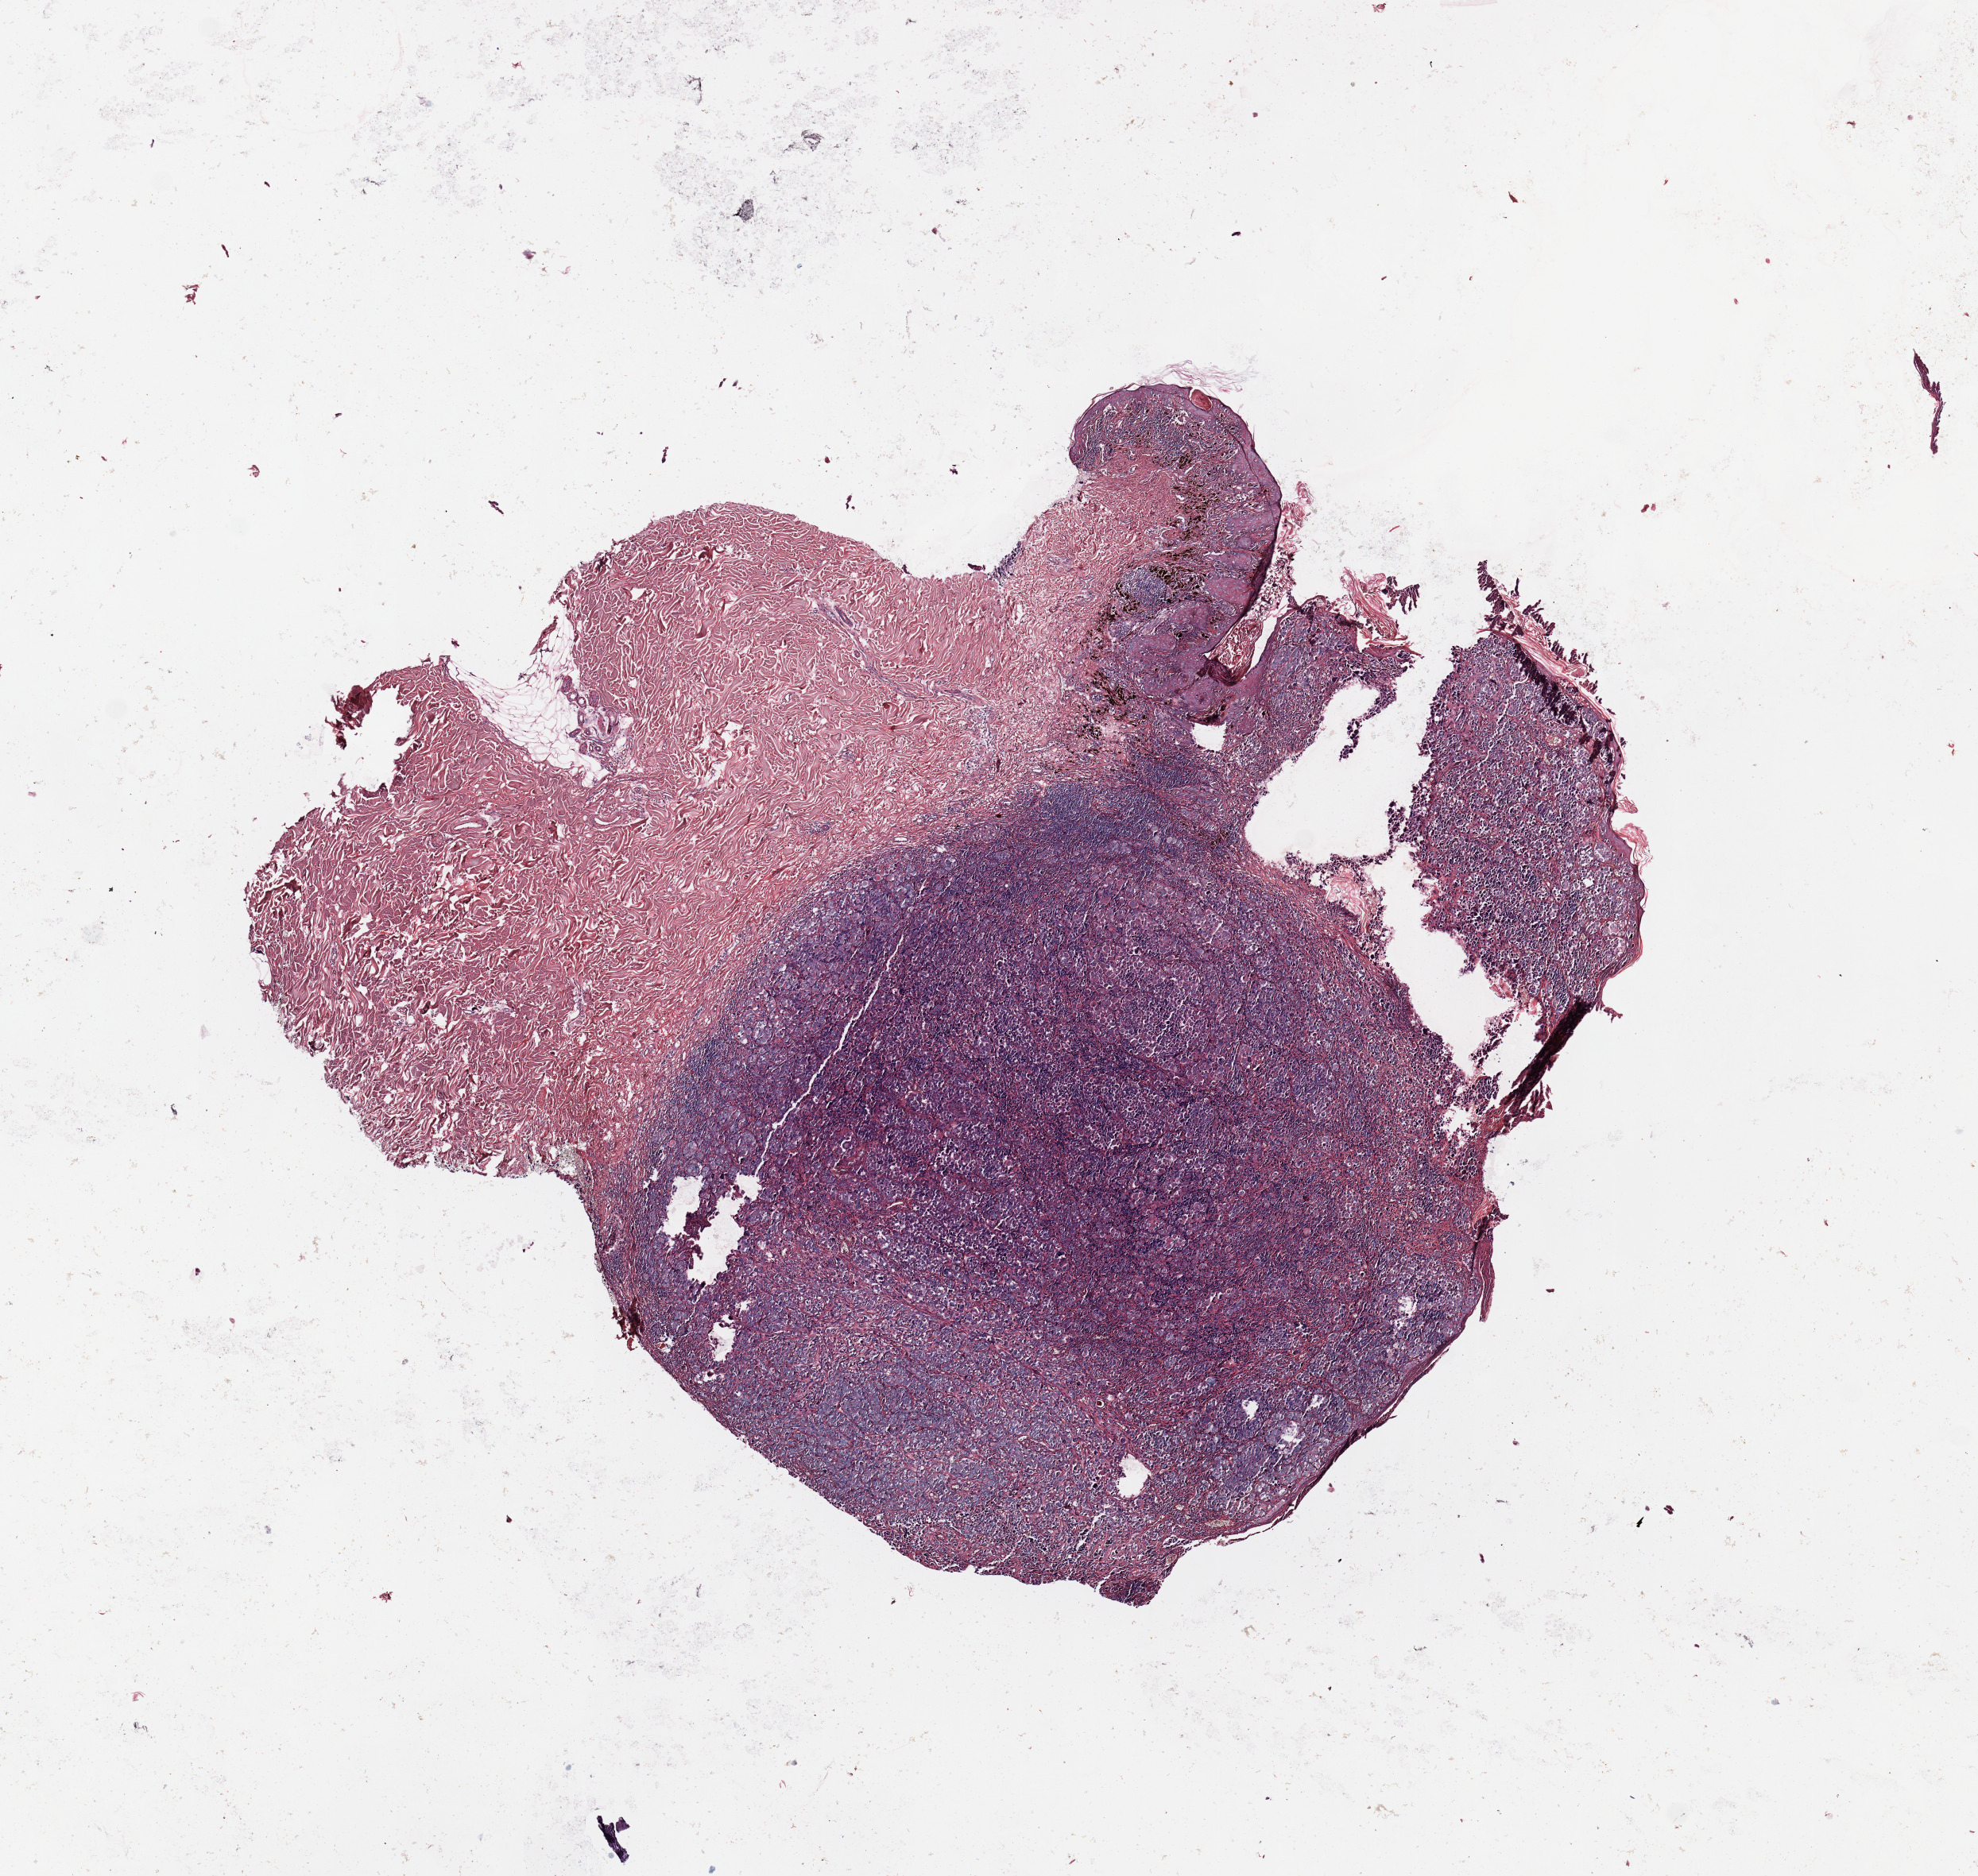
Hematoxylin and eosin (H&E) stained whole-slide image — low-resolution overview of the scanned area, about 9.8 x 9.3 mm, melanoma tumour tissue; sampled site not recorded. Patient: male, age 83 years.
- diagnosis: Malignant melanoma, NOS
- AJCC pathologic stage: IIB
- primary tumour site (as recorded): trunk